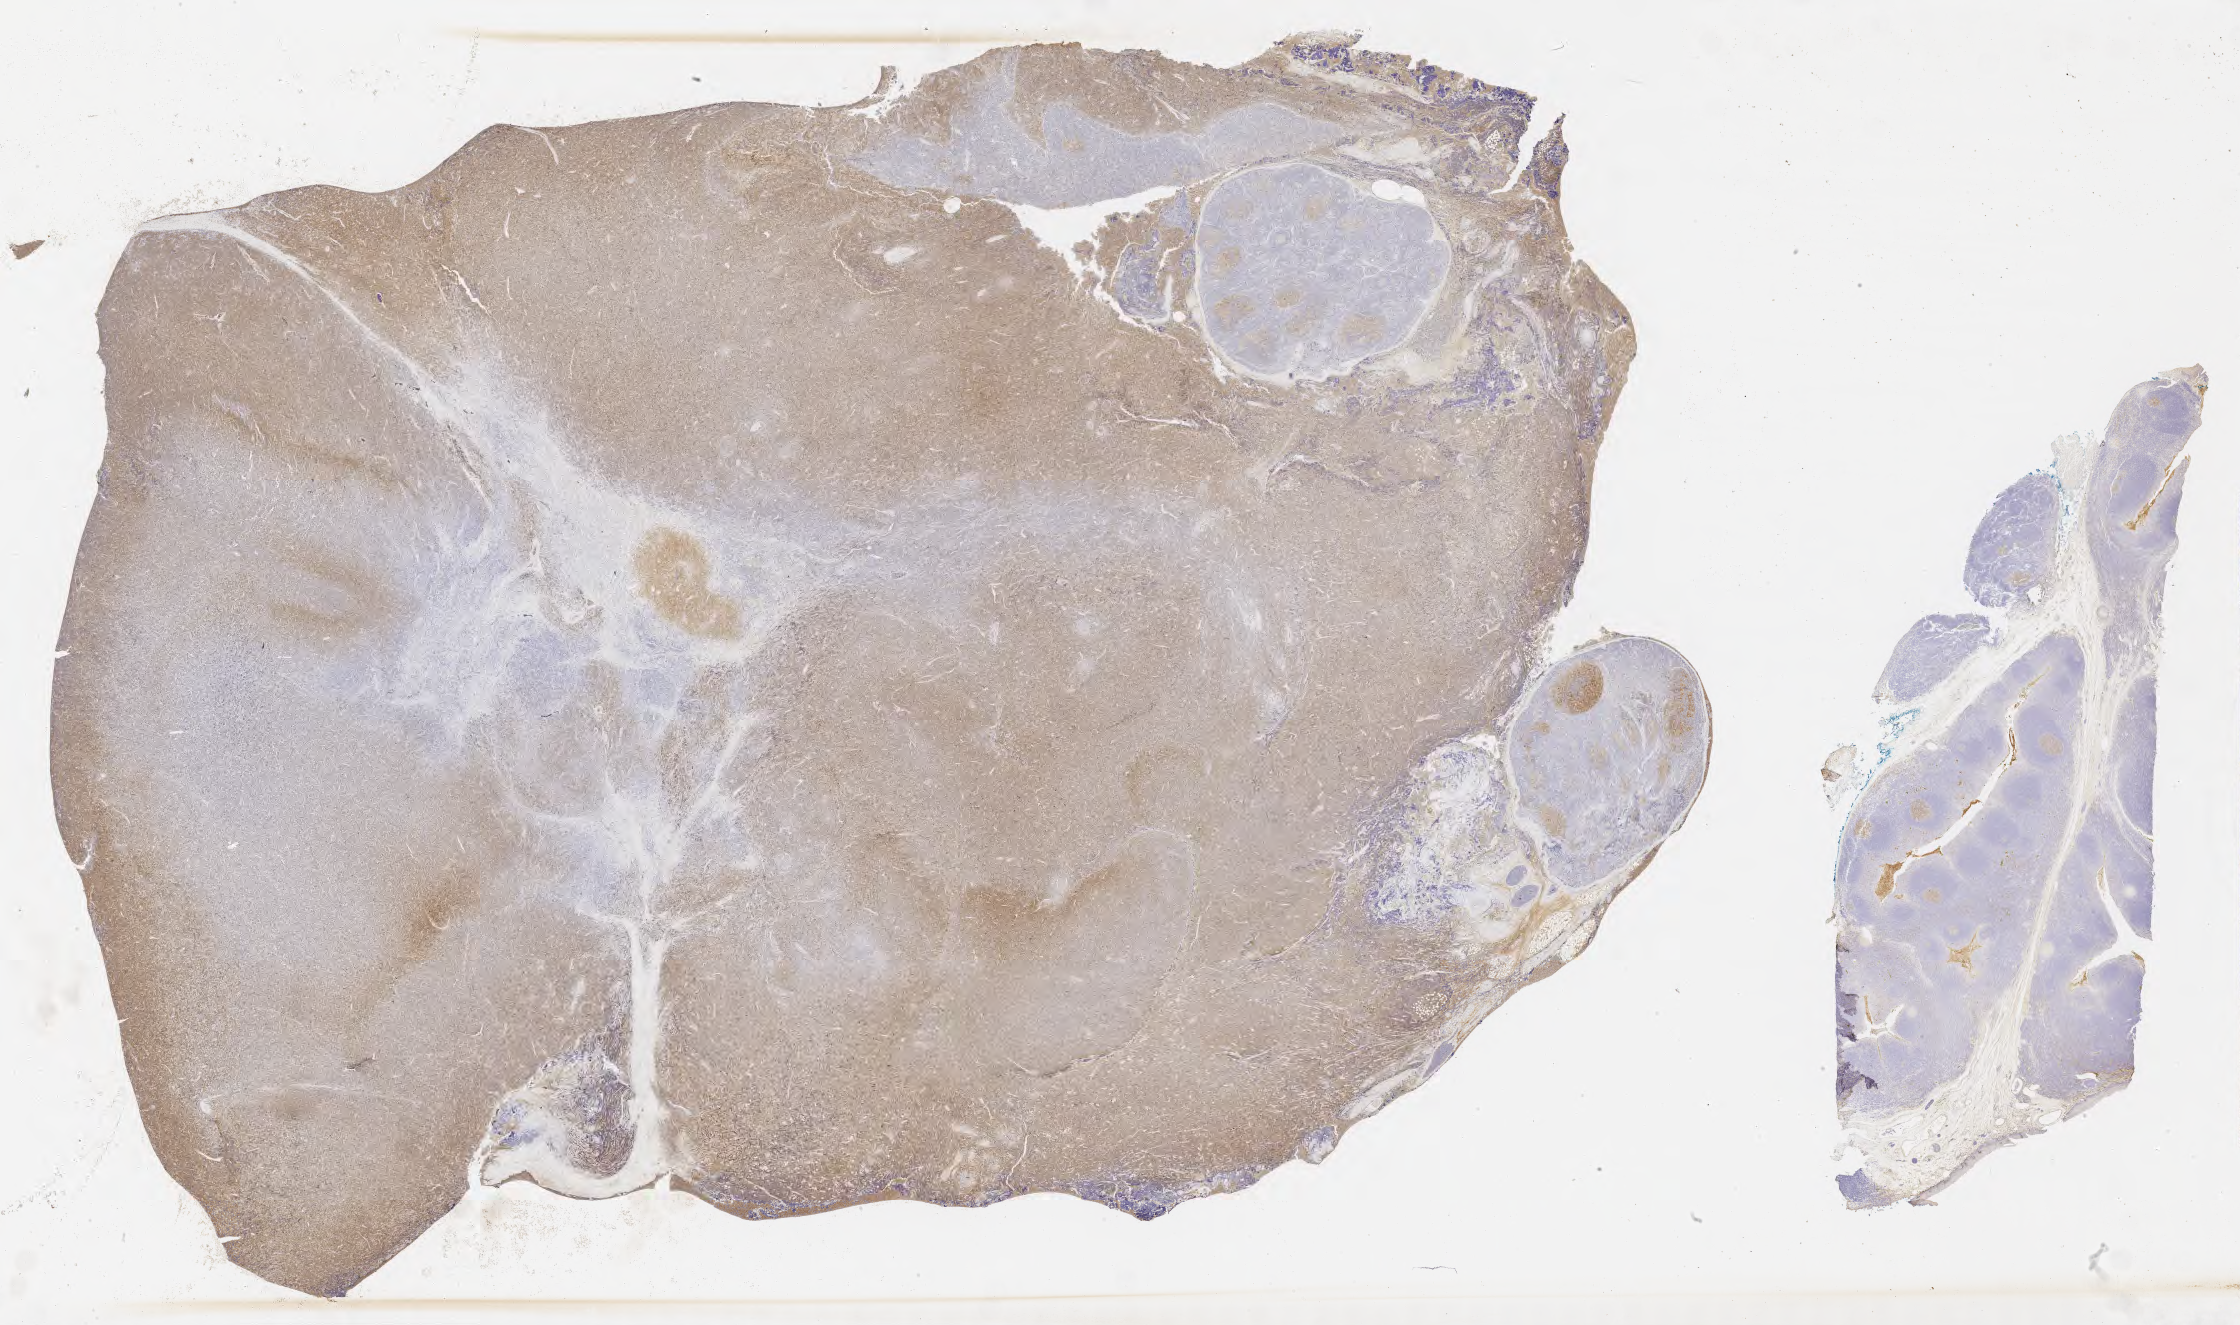
Immunohistochemistry (IHC) whole-slide image stained for CD10, a low-resolution overview of the entire scanned area, about 36.2 x 21.4 mm; specimen: tumor tissue; site: lymph node of head and neck. Male, age 3 years at initial diagnosis.
Diagnosis: Burkitt lymphoma, NOS.